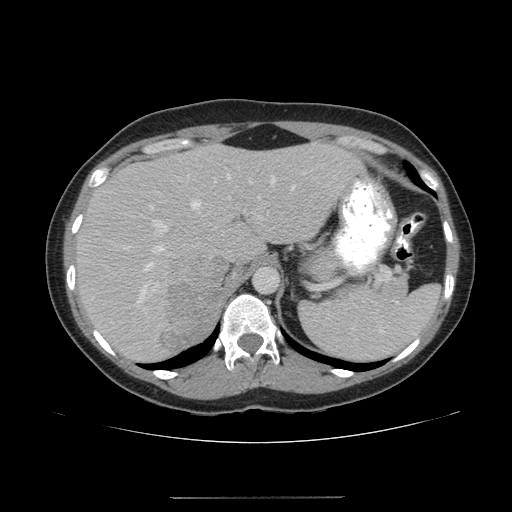
Contrast-enhanced abdominal CT, one axial slice. Position 123 of 161 along the scan axis. Reconstruction kernel STANDARD. 120 kVp. Intravenous contrast given. Soft-tissue window (W 400 / L 40 HU). 512 × 512 image matrix. Female patient. From the clinical record (not read from this slice): diagnosis: adrenocortical carcinoma; tumour side: right adrenal; tumour size at pathology: 9 cm; Ki-67 index: 14 %; stage (as recorded): 3.
Structures marked on this image (semi-automatically segmented with operator editing):
- mass: bounding box (x1, y1, x2, y2) in pixels: (164, 256, 236, 347)